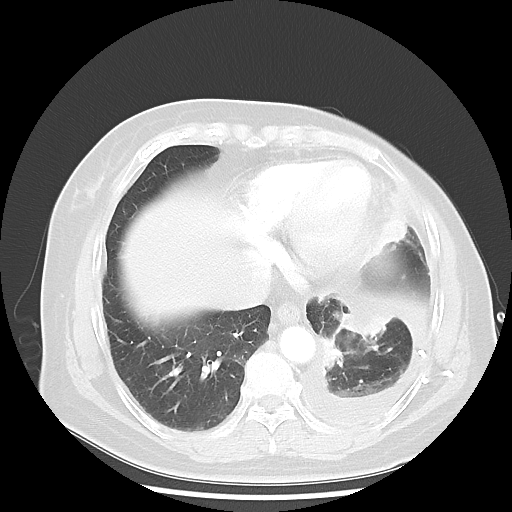
Chest CT, one axial slice. Position 13 of 48 along the scan axis. Lung window (W 1500 / L -600 HU). 512 × 512 image matrix. Patient: female, 63 years. From the clinical record (not read from this slice): clinical TNM (as recorded): T2 N0 M1.
Annotated regions visible in this slice (rectangle marked by the reading radiologist):
- lung tumour (recorded histology: adenocarcinoma): bounding box [x1, y1, x2, y2] px = [339, 299, 389, 350]